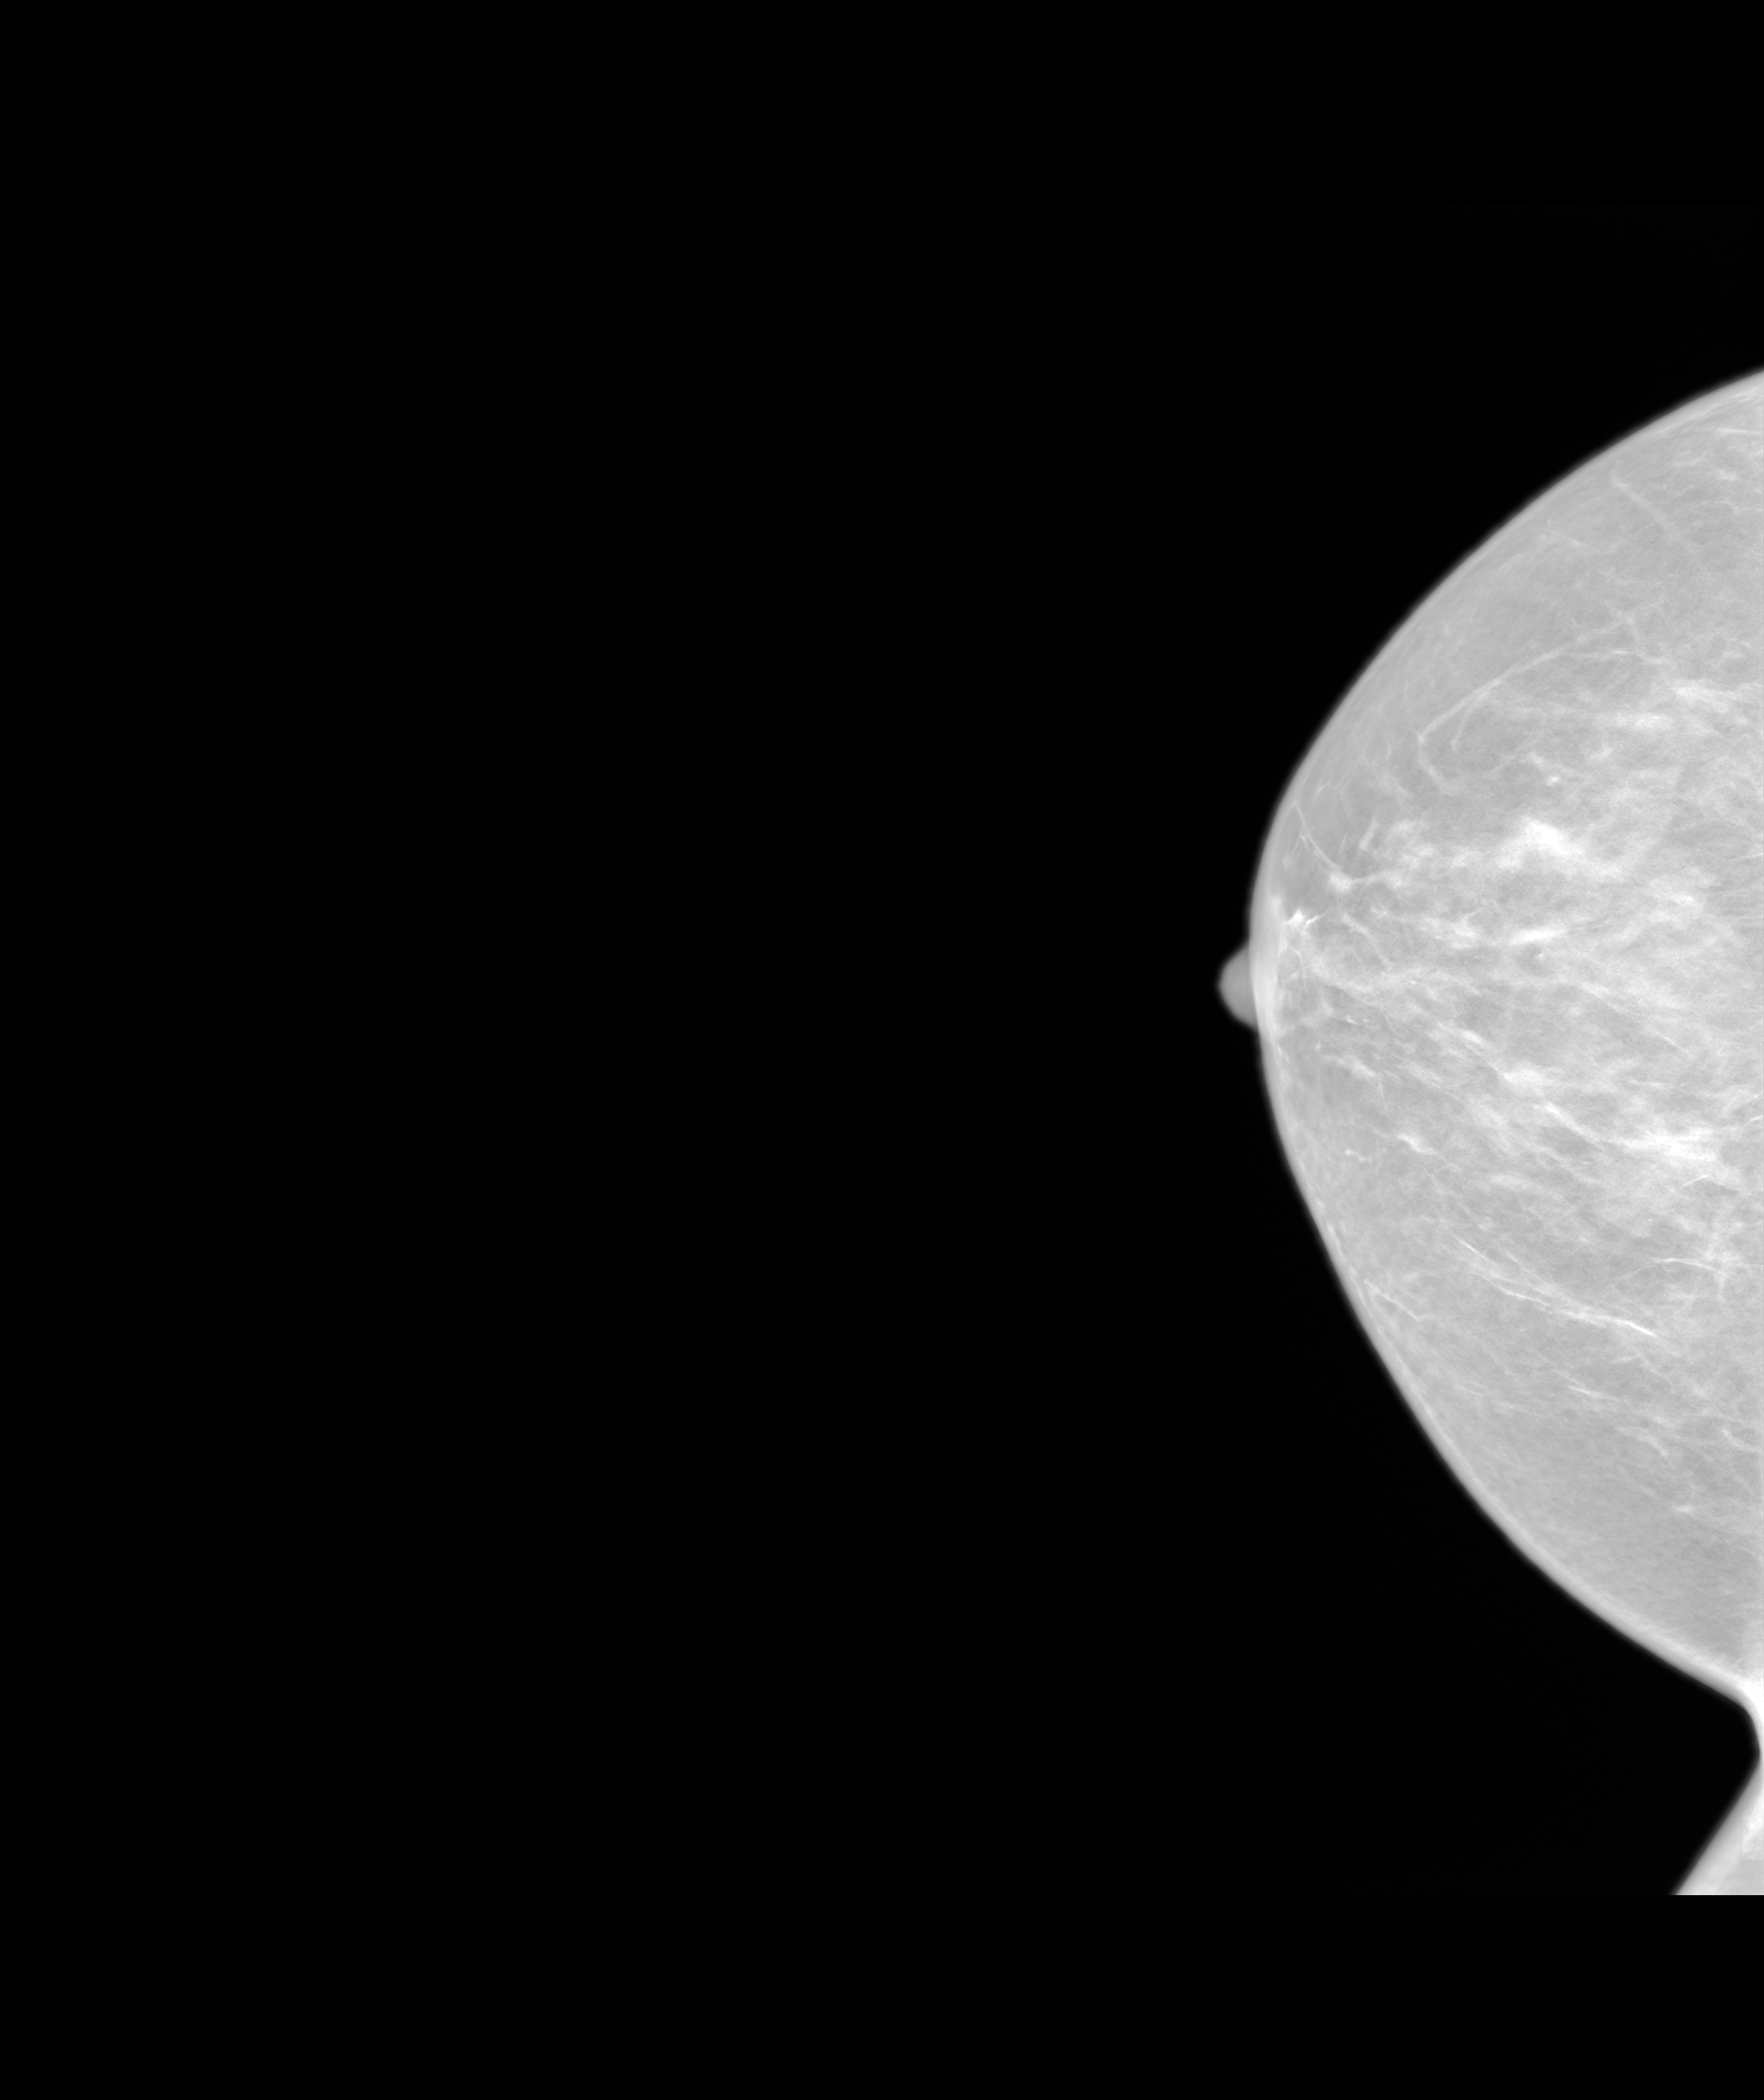
Annual screening mammography examination. Patient: female, 49 years.
Image type: synthesized 2-D view from tomosynthesis. Breast: right. Projection: CC view.